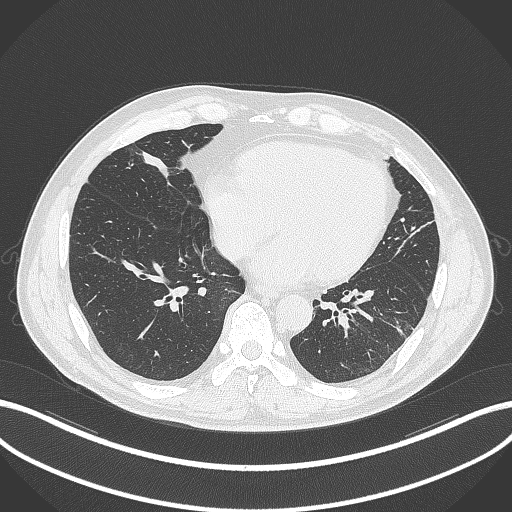
Chest CT, one axial slice; position 91 of 399 along the scan axis; reconstruction kernel B70f; lung window (W 1500 / L -600 HU); 1 mm slice thickness; 512 × 512 image matrix, field of view 400 × 400 mm. Male patient, age 59 years. From the clinical record (not read from this slice): clinical TNM (as recorded): T2a N1 M0.
Annotated regions visible in this slice (rectangle marked by the reading radiologist):
- lung tumour (recorded histology: adenocarcinoma): bounding box [x1, y1, x2, y2] px = [137, 143, 175, 183]